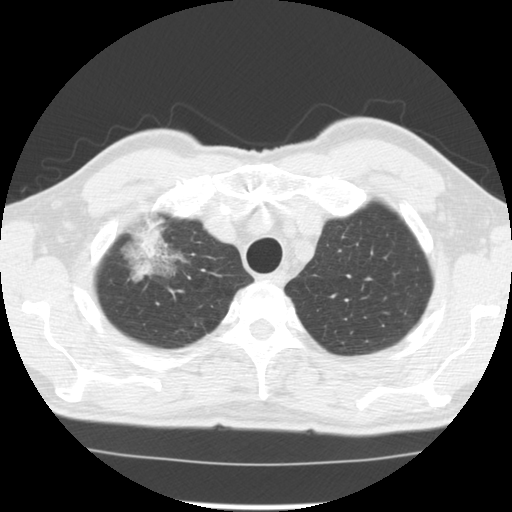
Low-dose screening chest CT, one axial slice. Position 107 of 128 along the scan axis. Reconstruction kernel STANDARD. Lung window (W 1500 / L -600 HU). 2.5 mm slice thickness. 512 × 512 image matrix.
Annotated regions visible in this slice (outlined manually by an expert reader):
- lesion 1 (tumor, upper lobe of right lung): bounding box (x1, y1, x2, y2) in pixels: (139, 229, 165, 257)